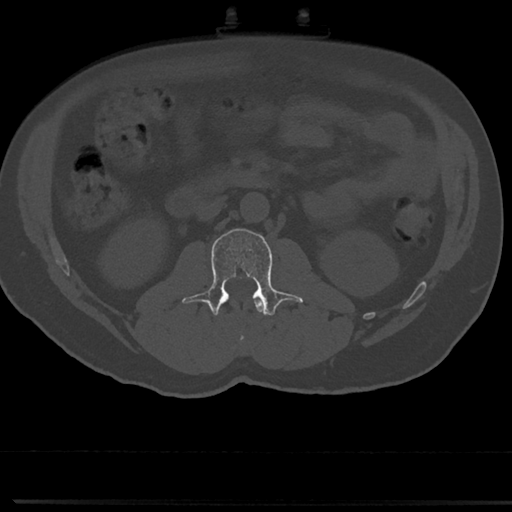
CT including the spine, one axial slice. Slice 24 of 817 in the series (ordered by position). Bone window (W 1800 / L 400 HU). 512 × 512 image matrix, field of view 355 × 355 mm. Patient: male, 61 years. Case-level facts recorded for this patient, not image findings: primary cancer: prostate.
Structures marked on this image (semi-automatic segmentation, software-assisted and operator-edited):
- L1 vertebra: box from (x=238, y=298) to (x=263, y=345) px
- L2 vertebra: (x=191, y=228)–(x=302, y=316)